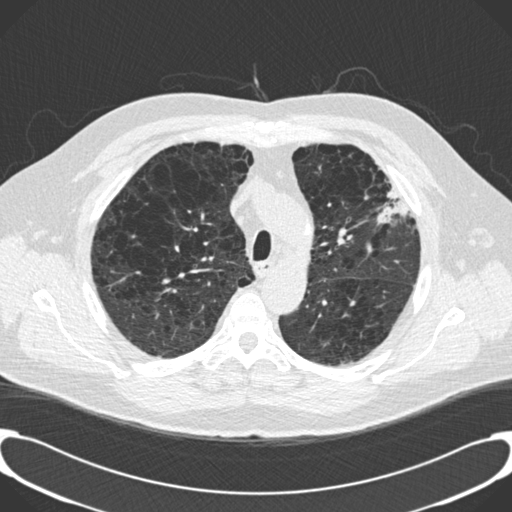
Low-dose screening chest CT, one axial slice. Position 147 of 189 along the scan axis. Lung window (W 1500 / L -600 HU). 2 mm slice thickness. 512 × 512 image matrix.
Outlined on this slice (expert manual segmentation):
- lesion 1 (tumor, upper lobe of left lung): bounding box <377,184,411,224> (left, top, right, bottom; pixels)